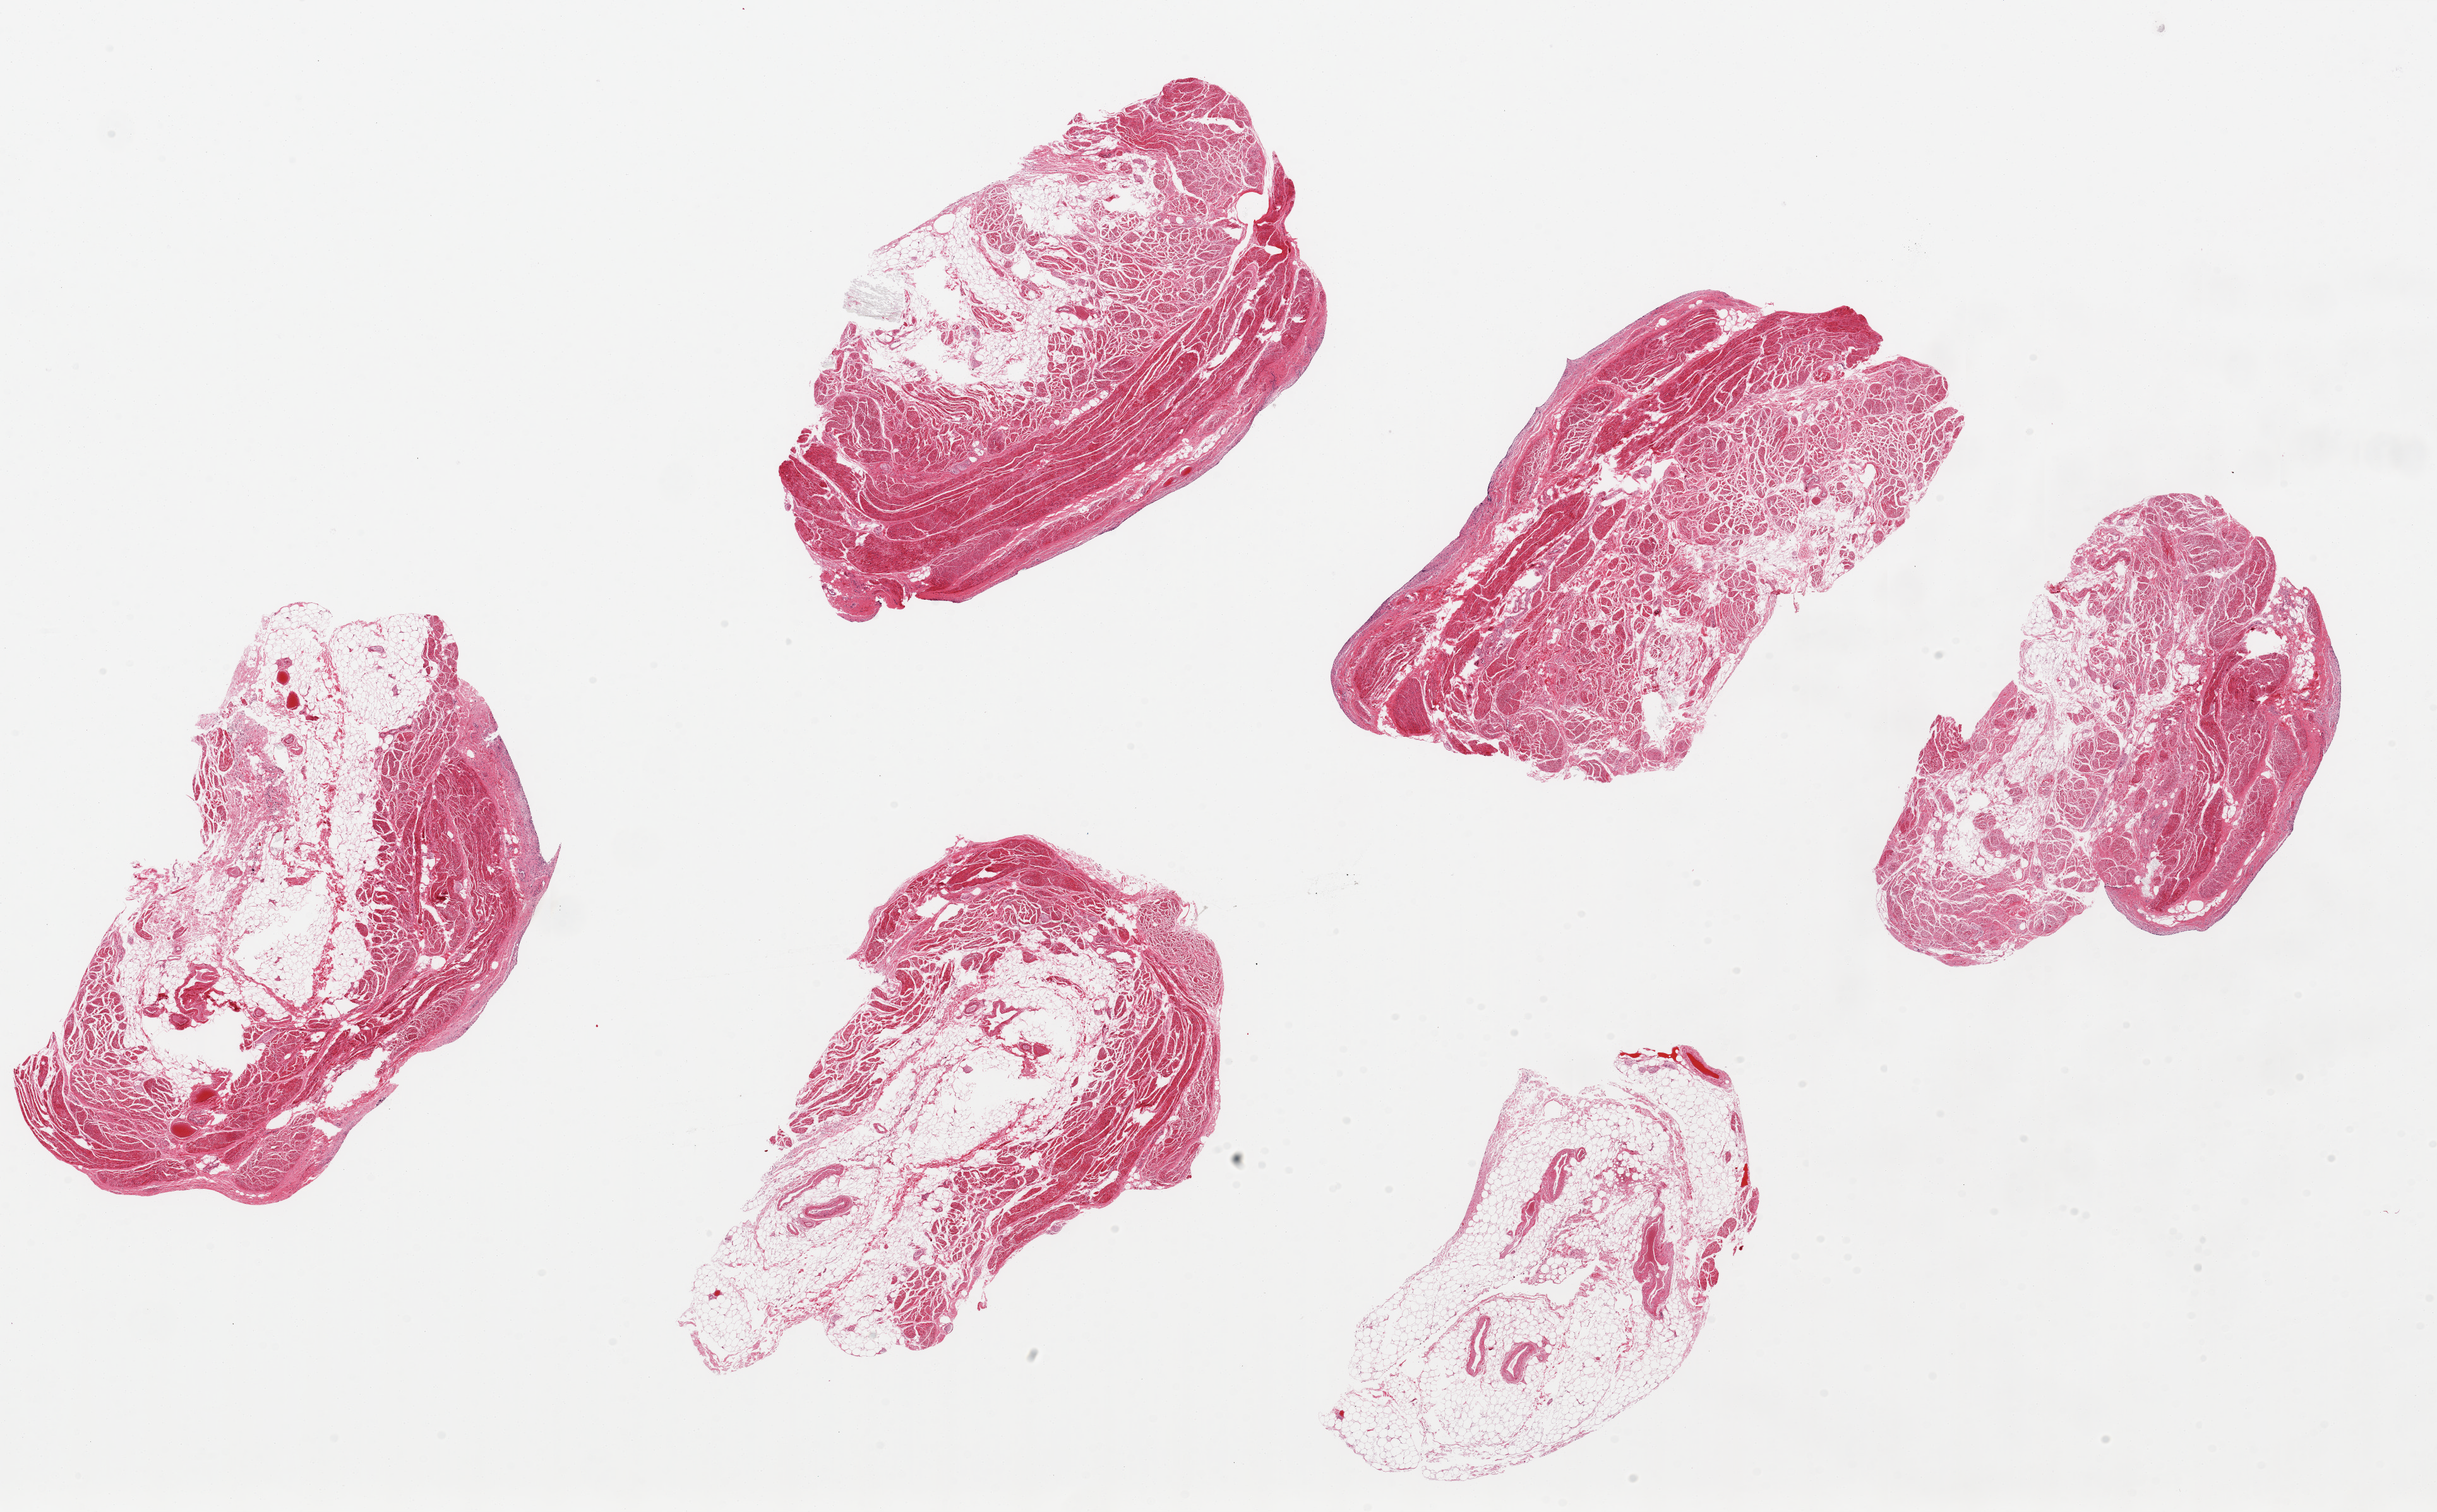
Whole-slide image, haematoxylin and eosin stain, brightfield, a low-resolution overview of the entire scanned area, about 30.5 x 18.9 mm (from a 20x scan); PAXgene-fixed paraffin-embedded (PFPE) section; target tissue: urinary bladder; donor tissue sample. Male donor.
Reviewer comment on this tissue sample: 6 pieces, ~7x4mm. Urothelium completely sloughed, badly autolyzed.